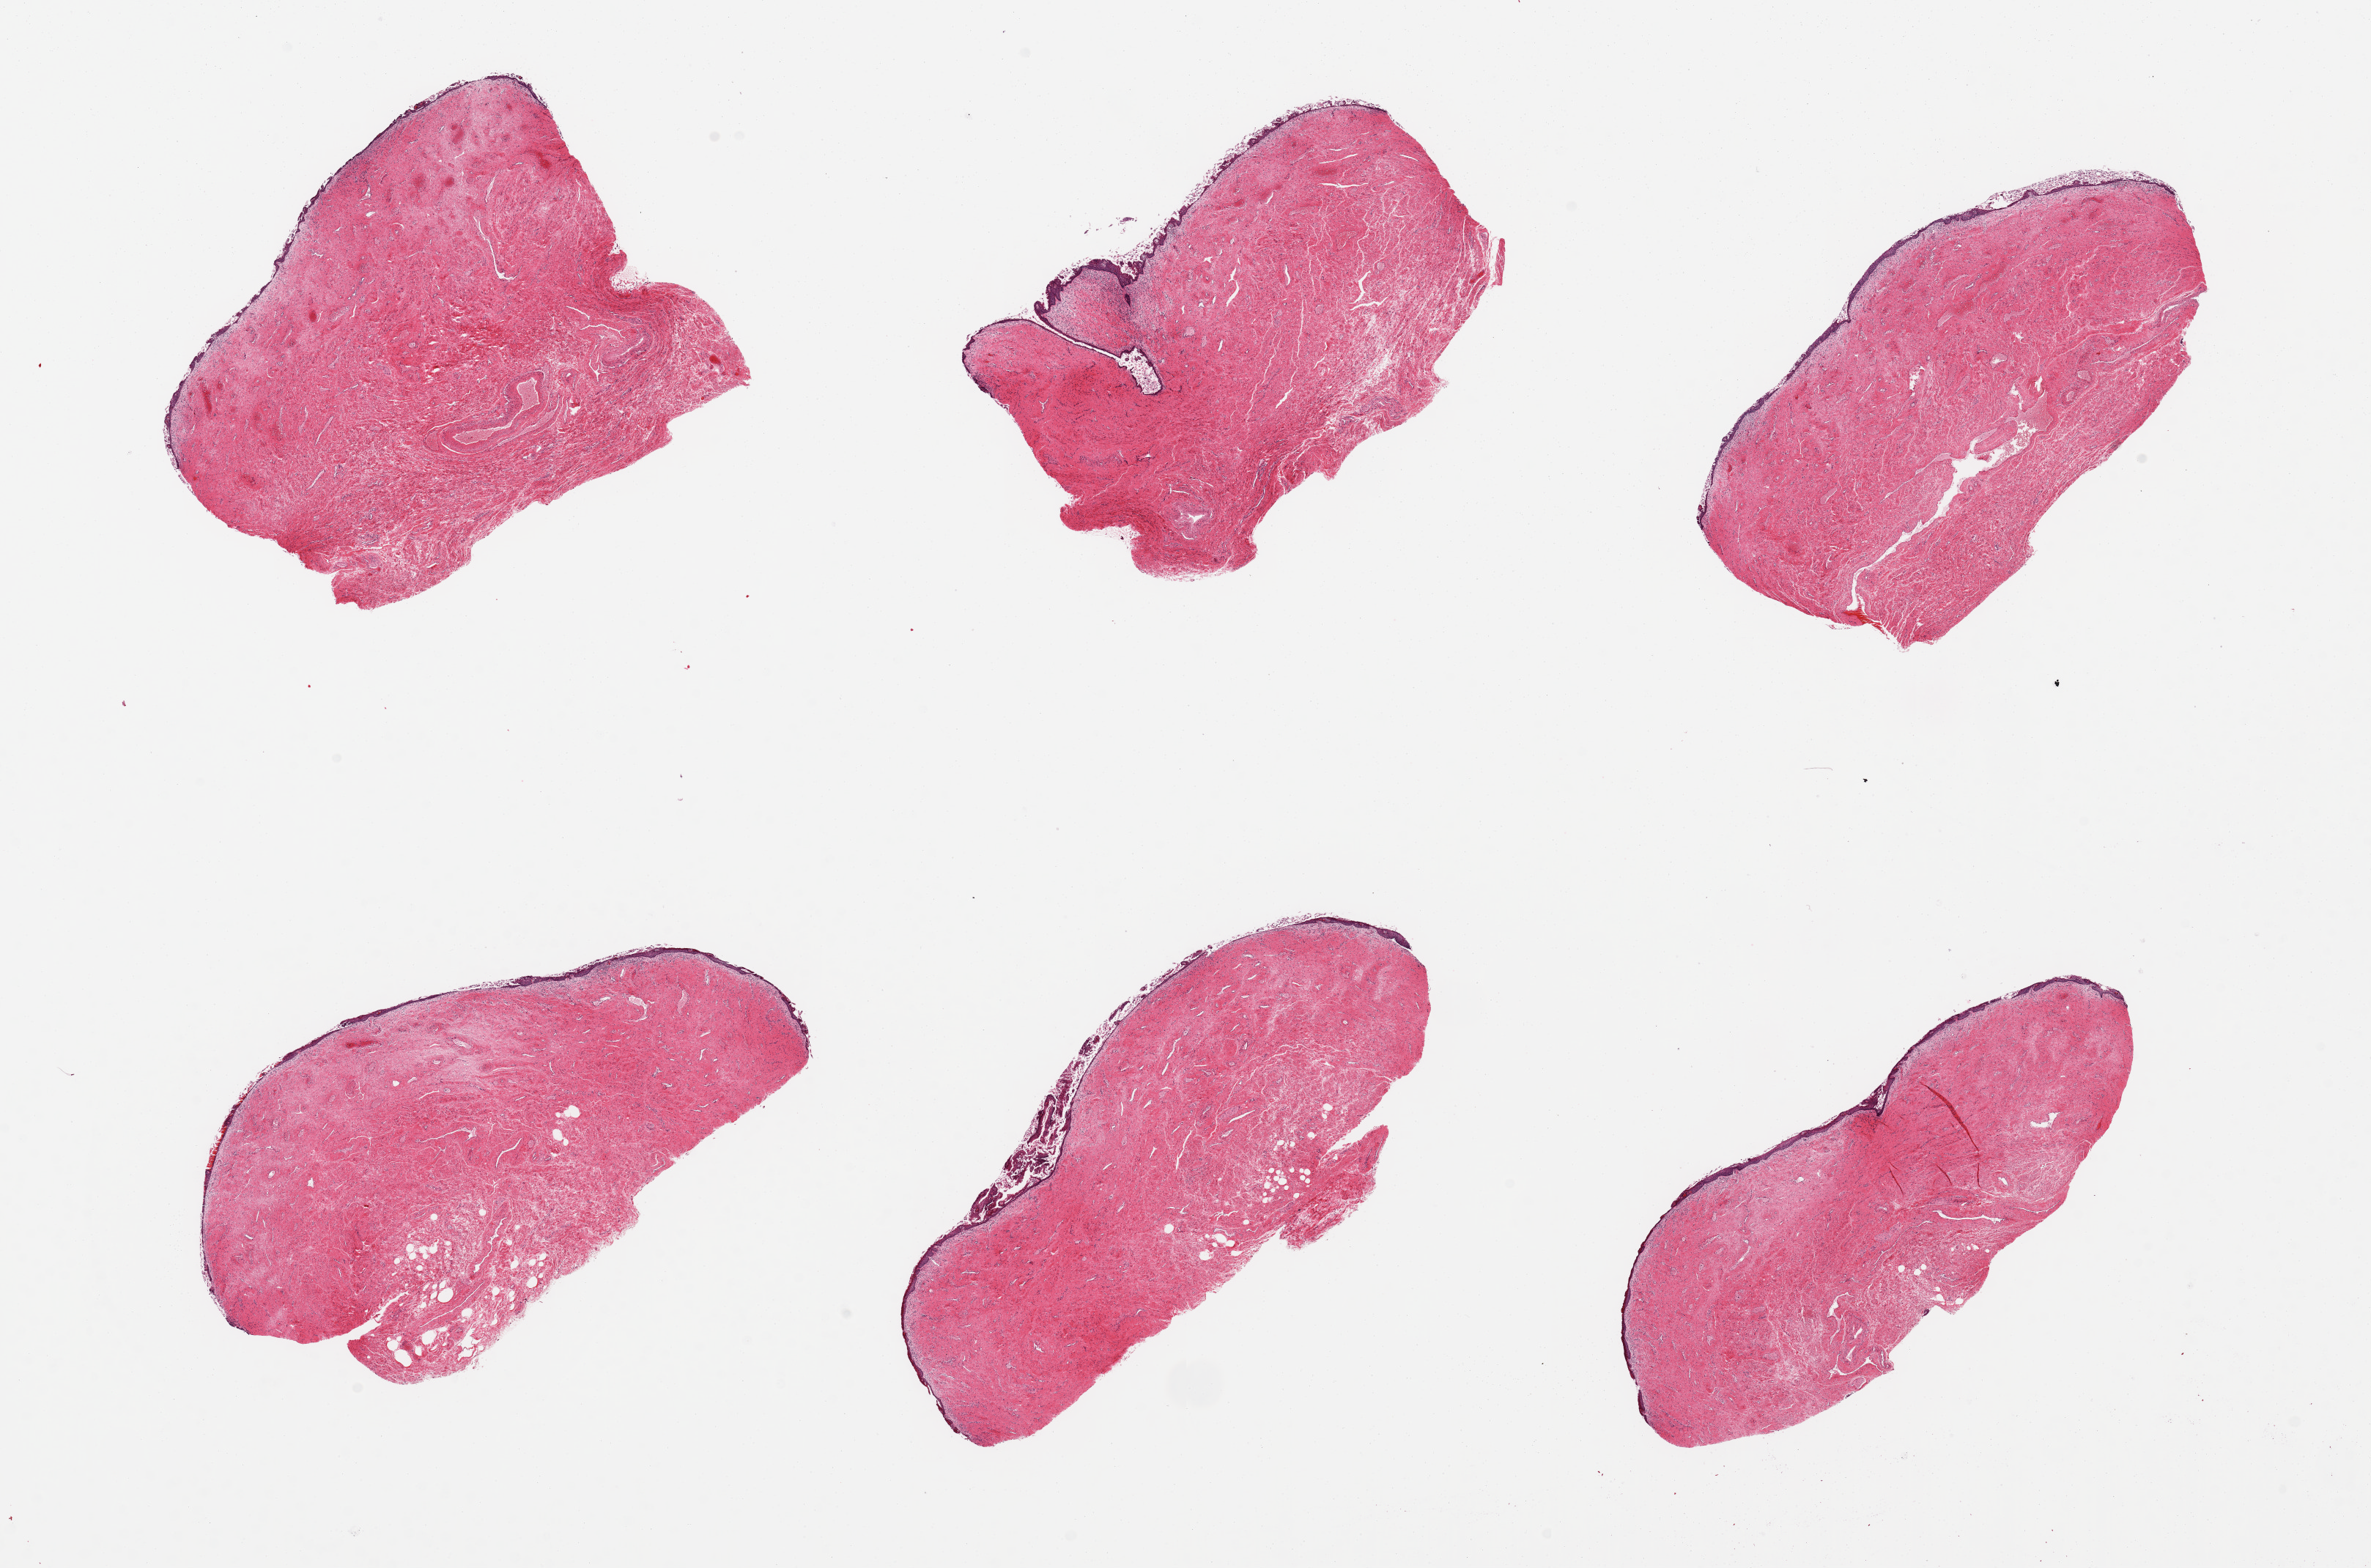
Haematoxylin and eosin whole-slide image — a low-resolution overview of the entire scanned area, about 25.6 x 16.9 mm (slide scanned at 20x). PAXgene-fixed paraffin-embedded (PFPE) section. Section of vagina (target tissue). Tissue donor sample. Donor sex: female.
Review note (as recorded): 6 pieces, squamous epithelium is largely denuded/sloughing.